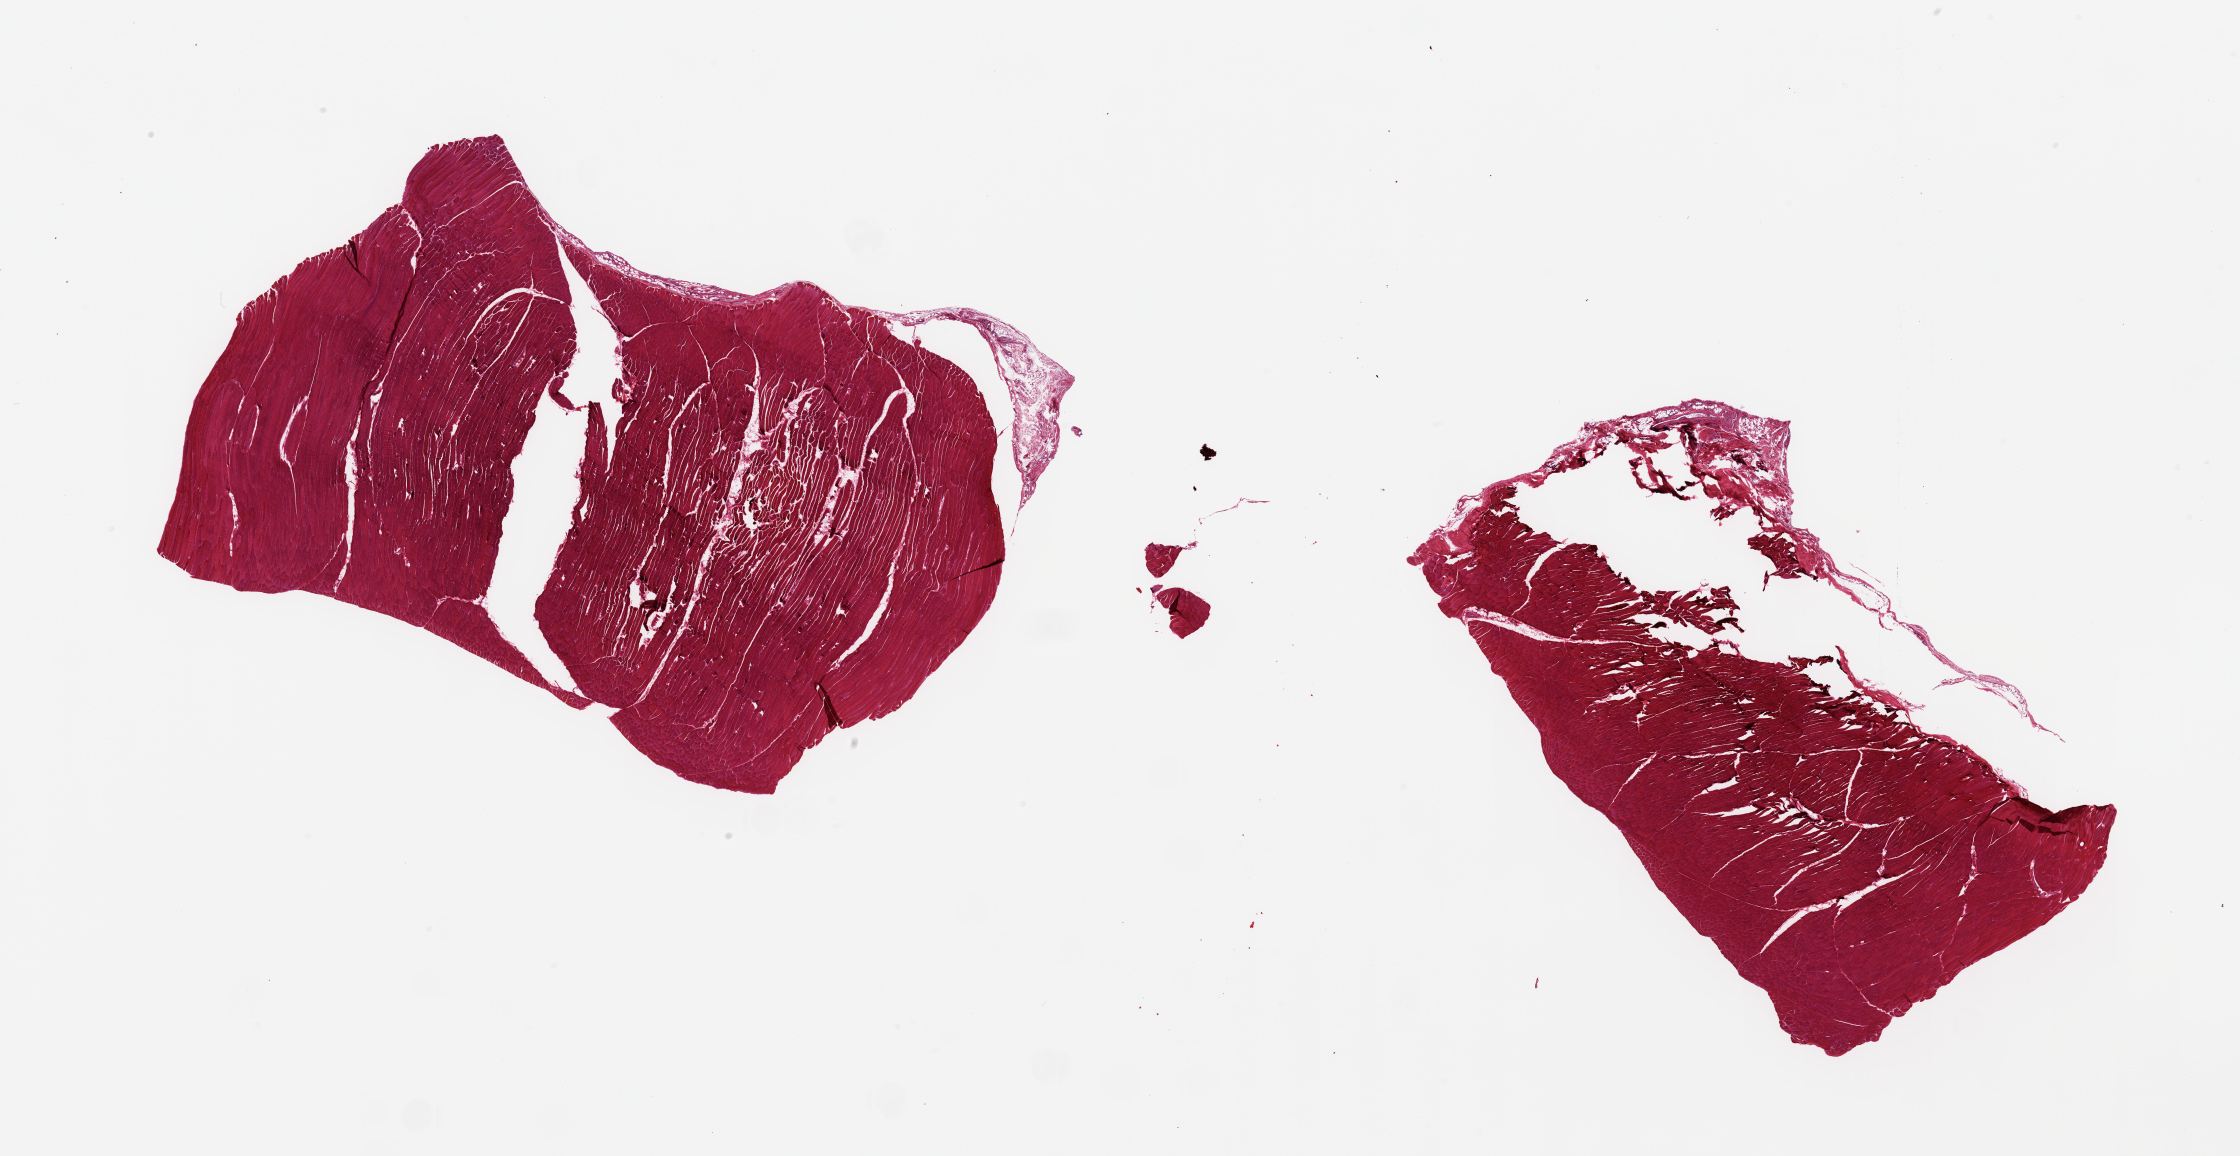
Digitized H&E-stained section, brightfield, shown as a low-resolution overview of the whole scanned area (about 35.4 x 18.3 mm, slide scanned at 20x). PAXgene-fixed, paraffin-embedded tissue. Target tissue: skeletal muscle. Tissue donor sample. Donor sex: male.
* pathologist's review note for this sample: 2 pieces, trace interstitial fat